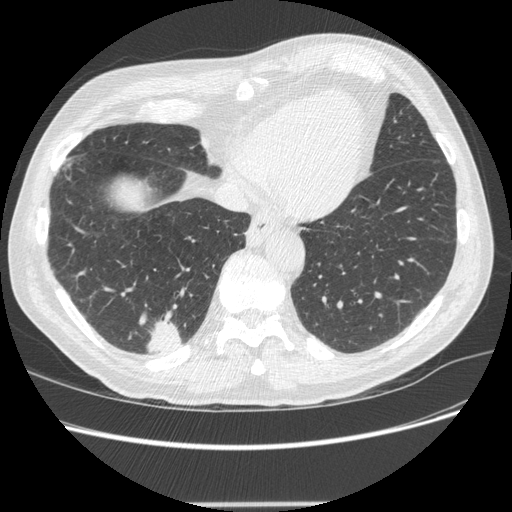
Low-dose screening chest CT, one axial slice; slice 64 of 245 in the series (ordered by position); reconstruction kernel STANDARD; 120 kVp; lung window (W 1500 / L -600 HU); 1.25 mm slice thickness; 512 × 512 image matrix, field of view 372 × 372 mm.
Outlined on this slice (outlined manually by an expert reader):
- lesion 1 (tumor, lower lobe of right lung): bounding box [x1, y1, x2, y2] px = [147, 321, 182, 354]